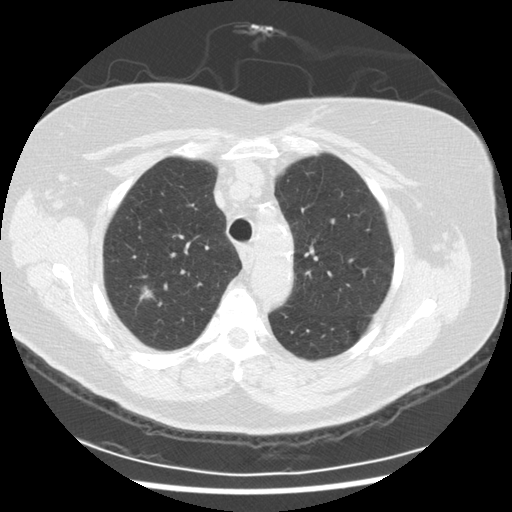
Low-dose screening chest CT, one axial slice; reconstruction kernel STANDARD; 120 kVp; lung window (W 1500 / L -600 HU); 2.5 mm slice thickness; 512 × 512 image matrix.
Outlined on this slice (outlined manually by an expert reader):
- lesion 1 (tumor, upper lobe of right lung): box from (x=140, y=286) to (x=153, y=301) px